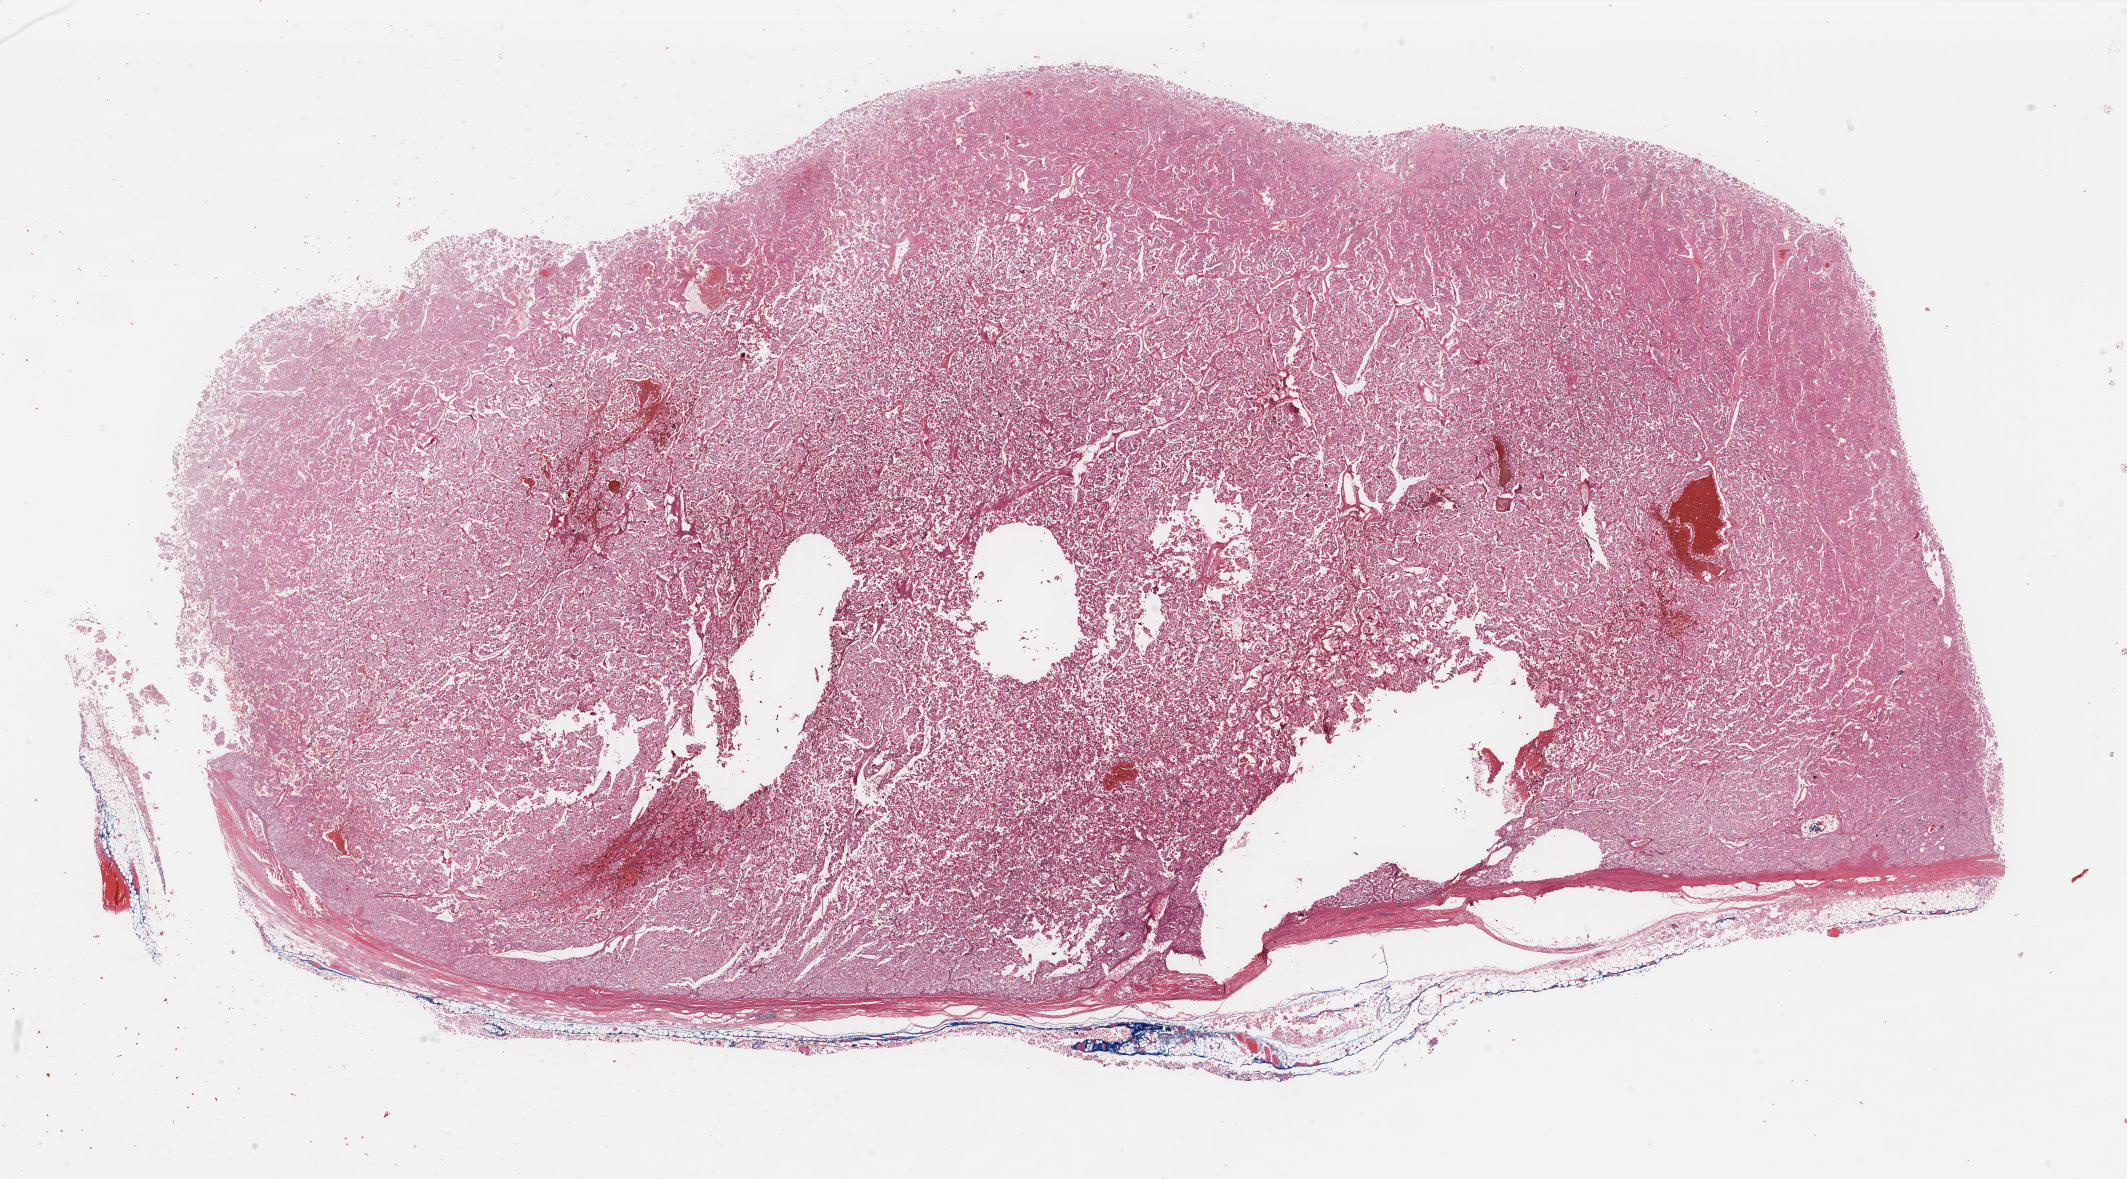
Digitized H&E tissue section (whole slide), low-resolution overview of the scanned area, about 33.7 x 18.7 mm (acquisition: 40x scan). Formalin-fixed paraffin-embedded (FFPE) diagnostic section. Sample: primary tumour, kidney. Female, age 44 years at initial diagnosis. Slide review estimates, as recorded: tumour cells 80%, tumour nuclei 80%, normal cells 0%, stromal cells 18%, necrosis 2%. Infiltration values recorded for this section: lymphocyte infiltration 3%, monocyte infiltration 1%, neutrophil infiltration 1%.
- diagnosis: Renal cell carcinoma, chromophobe type
- laterality: right
- AJCC pathologic stage: II (5th edition)